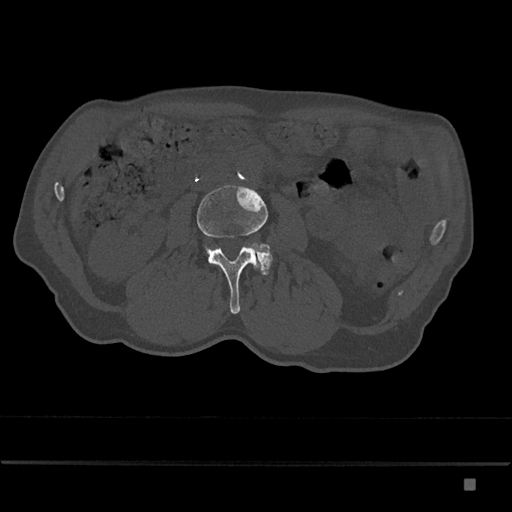
CT including the spine, one axial slice; slice 397 of 797 in the series (ordered by position); reconstruction kernel Br40s/3; 120 kVp; bone window (W 1800 / L 400 HU); 512 × 512 image matrix, field of view 390 × 390 mm. Patient: male, 72 years. Case-level facts recorded for this patient, not image findings: primary cancer: prostate.
Annotated regions visible in this slice (semi-automatically segmented with operator editing):
- L3 vertebra: bounding box <197,185,269,314> (left, top, right, bottom; pixels)
- L4 vertebra: <250,244,272,275>